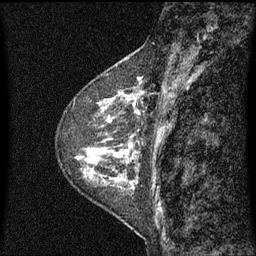
Breast MRI (dynamic contrast-enhanced), one sagittal slice. Slice 23 of 60 in the series (ordered by position). Dynamic contrast-enhanced series, image 2 of 3 at this slice position (ordered by acquisition). 1.5 T. TE 4.2 ms, TR 8 ms. 2 mm slice thickness. 256 × 256 image matrix, field of view 200 × 200 mm. Patient: female, 48 years.
Annotated regions visible in this slice (semi-automatically segmented with operator editing):
- analysis volume of interest (the breast-tissue region the enhancement analysis was run in; not a lesion): bounding box <103,74,145,139> (left, top, right, bottom; pixels)
- tumour enhancement mask (voxels above the 70 % enhancement threshold inside the analysis volume of interest): <106,76,145,139>